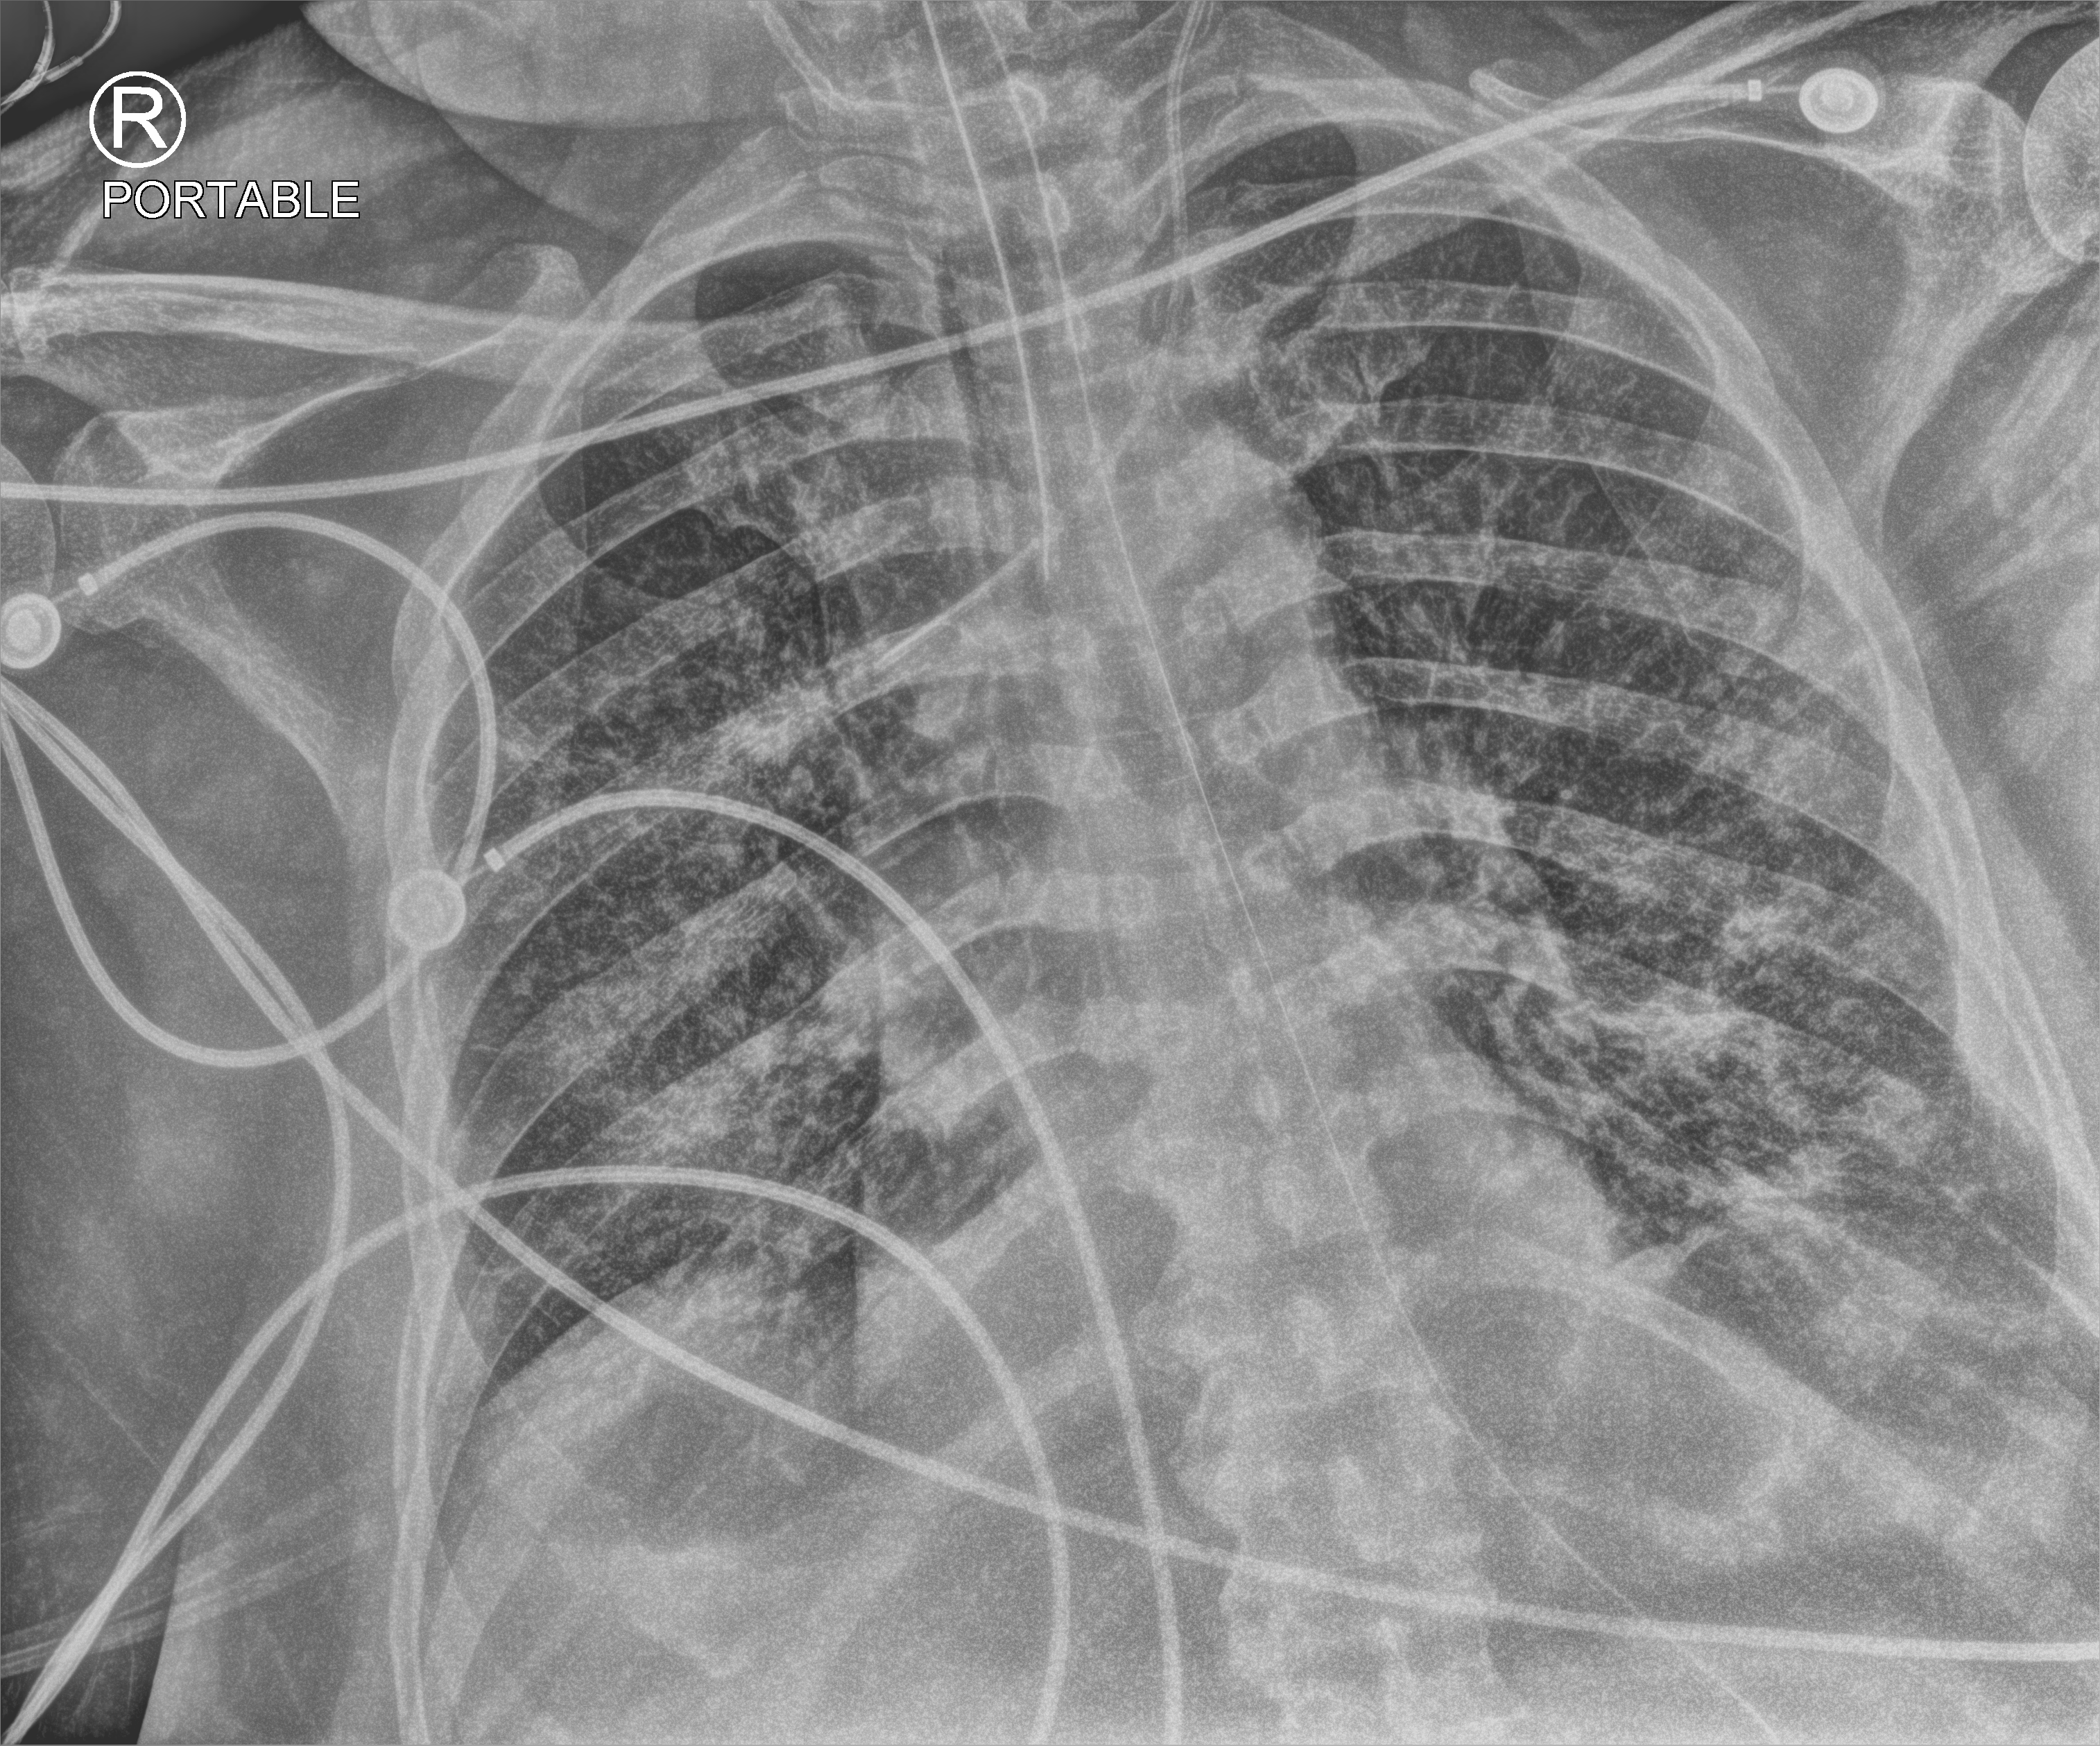
Chest X-ray (portable). Adult patient hospitalised with COVID-19, age 18–59 years.
Admission-level facts for this patient (not findings on this image; timing relative to this image not recorded): mechanically ventilated during this hospital stay: yes.